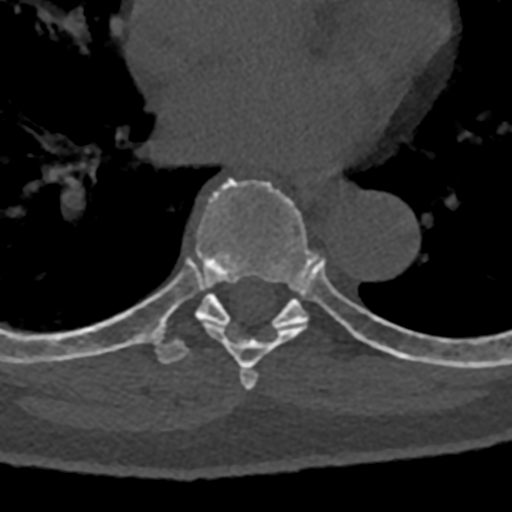
CT including the spine, one axial slice; slice 741 of 797 in the series (ordered by position); 120 kVp; bone window (W 1800 / L 400 HU); 0.5 mm slice thickness; 512 × 512 image matrix. Male patient, age 74 years. From the clinical record (not read from this slice): primary cancer: renal; vertebrae with lytic lesions (as recorded): T10, L1, L2, L3, L4, L5.
Outlined on this slice (semi-automatically segmented with operator editing):
- T6 vertebra: box from (x=240, y=370) to (x=258, y=382) px
- T7 vertebra: (x=143, y=177)–(x=394, y=390)
- T8 vertebra: (x=70, y=291)–(x=432, y=364)